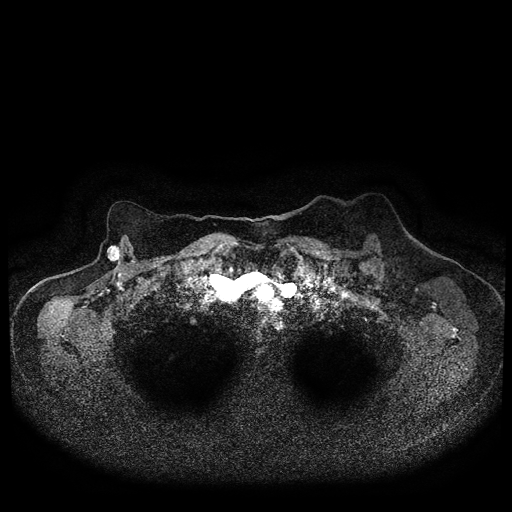
Breast MRI (dynamic contrast-enhanced, multi-phase), one axial slice; position 79 of 116 along the scan axis; dynamic contrast-enhanced series, time point 2 of 5 at this slice position (early post-contrast); 1.5 T; TE 2.7 ms, TR 5.4 ms; 512 × 512 image matrix, field of view 340 × 340 mm. Female patient, age 72 years.
Outlined on this slice (semi-automatically segmented with operator editing):
- breast lesion (labelled 'tumour' in the annotation; benign lesions carry a separate 'benign' label): bounding box [x1, y1, x2, y2] px = [106, 244, 122, 264]